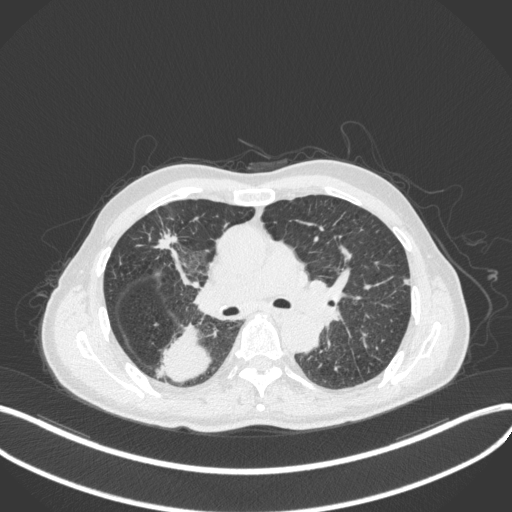
Chest CT, one axial slice. Position 274 of 423 along the scan axis. 120 kVp. Lung window (W 1500 / L -600 HU). 1 mm slice thickness. 512 × 512 image matrix, field of view 400 × 400 mm. Male patient, age 79 years. From the clinical record (not read from this slice): clinical TNM (as recorded): T3 N0 M0.
Outlined on this slice (rectangle marked by the reading radiologist):
- lung tumour (recorded histology: adenocarcinoma): bounding box (x1, y1, x2, y2) in pixels: (155, 322, 215, 384)